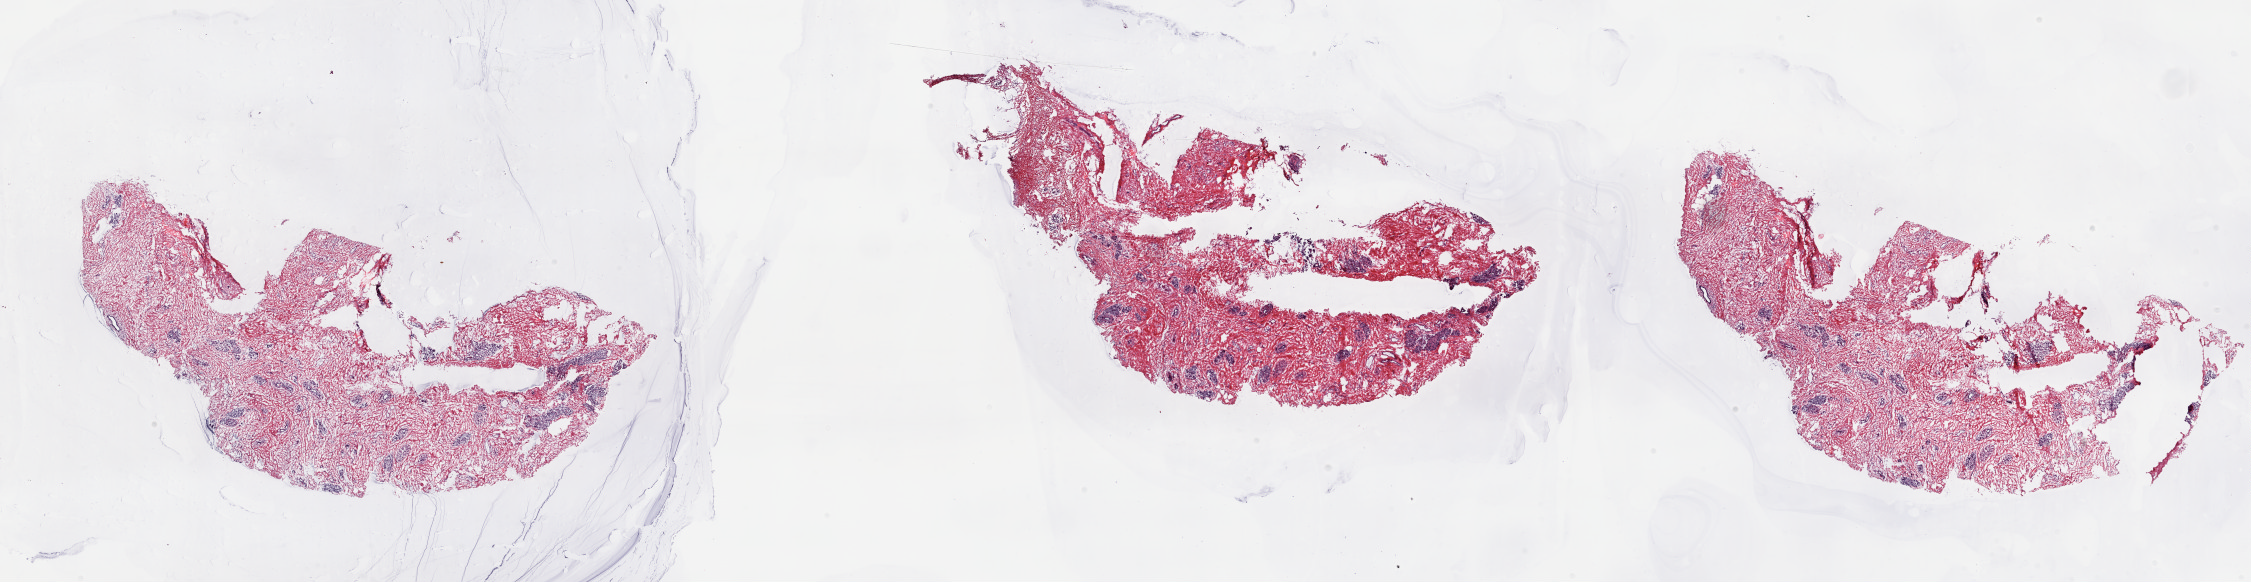
Digitized H&E tissue section (whole slide) — low-resolution overview of the scanned area, about 35.7 x 9.2 mm (from a 20x scan); frozen section; sample: solid tissue normal (non-tumour tissue), breast. Female, age 52 years at initial diagnosis. Slide review estimates, as recorded: tumour cells 0%, tumour nuclei 0%, normal cells 20%, stromal cells 80%, necrosis 0%. Inflammatory infiltration, as recorded: lymphocyte infiltration 2%, monocyte infiltration 2%, neutrophil infiltration 0%.
This section: solid tissue normal sample (biorepository sample class). Patient diagnosis: Infiltrating duct carcinoma, NOS.